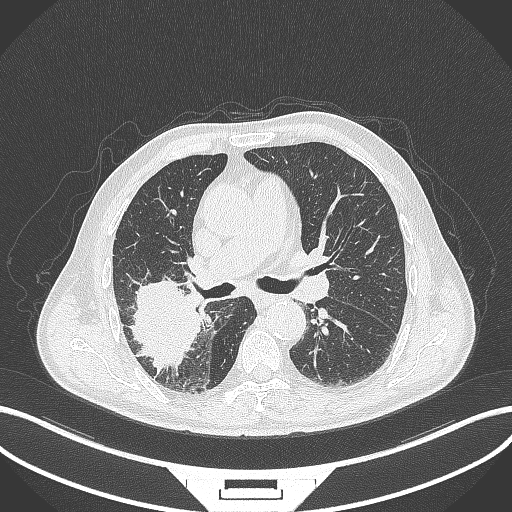
Chest CT, one axial slice. Position 242 of 429 along the scan axis. Reconstruction kernel B70f. Lung window (W 1500 / L -600 HU). 512 × 512 image matrix, field of view 400 × 400 mm. Patient: male, 72 years. From the clinical record (not read from this slice): clinical TNM (as recorded): T3 N2 M0.
Annotated regions visible in this slice (bounding box drawn by a radiologist):
- lung tumour (recorded histology: adenocarcinoma): bounding box [x1, y1, x2, y2] px = [124, 276, 205, 374]